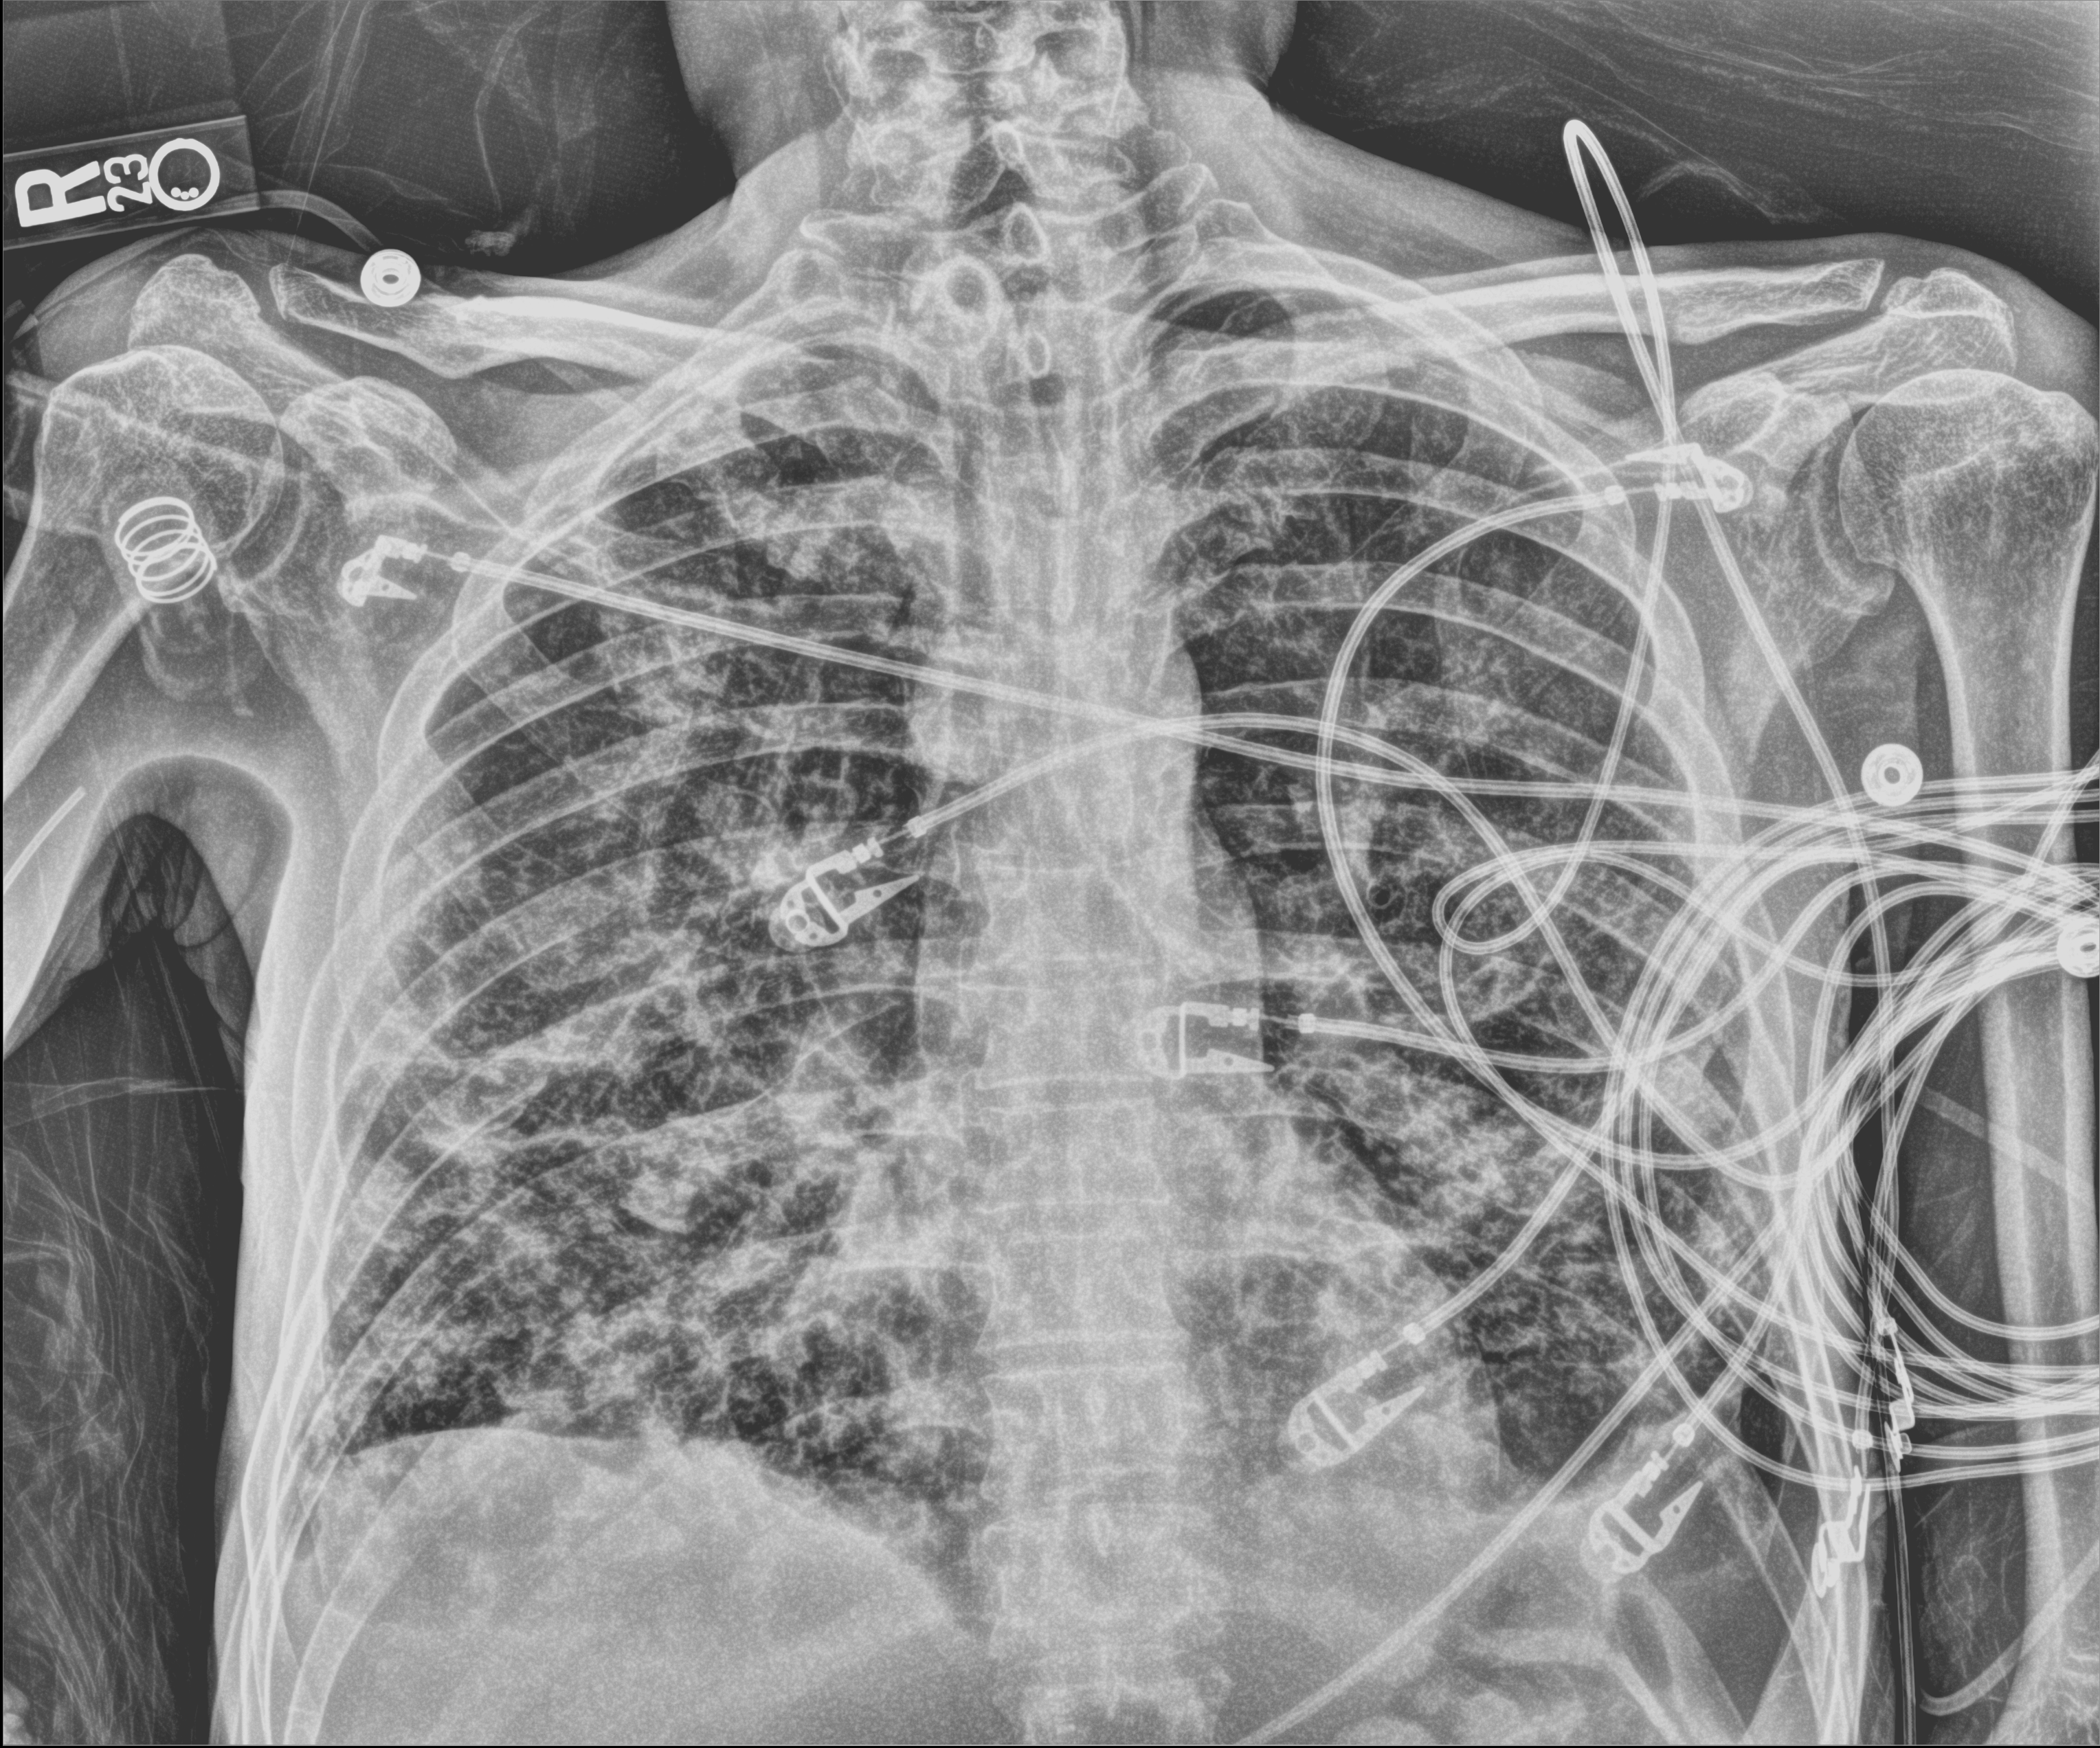
Bedside chest radiograph (computed radiography); anteroposterior (AP) projection. Patient hospitalised with COVID-19; male, aged 18–59 years.
Admission-level facts for this patient (not findings on this image; timing relative to this image not recorded): admitted to intensive care during this hospital stay: yes.